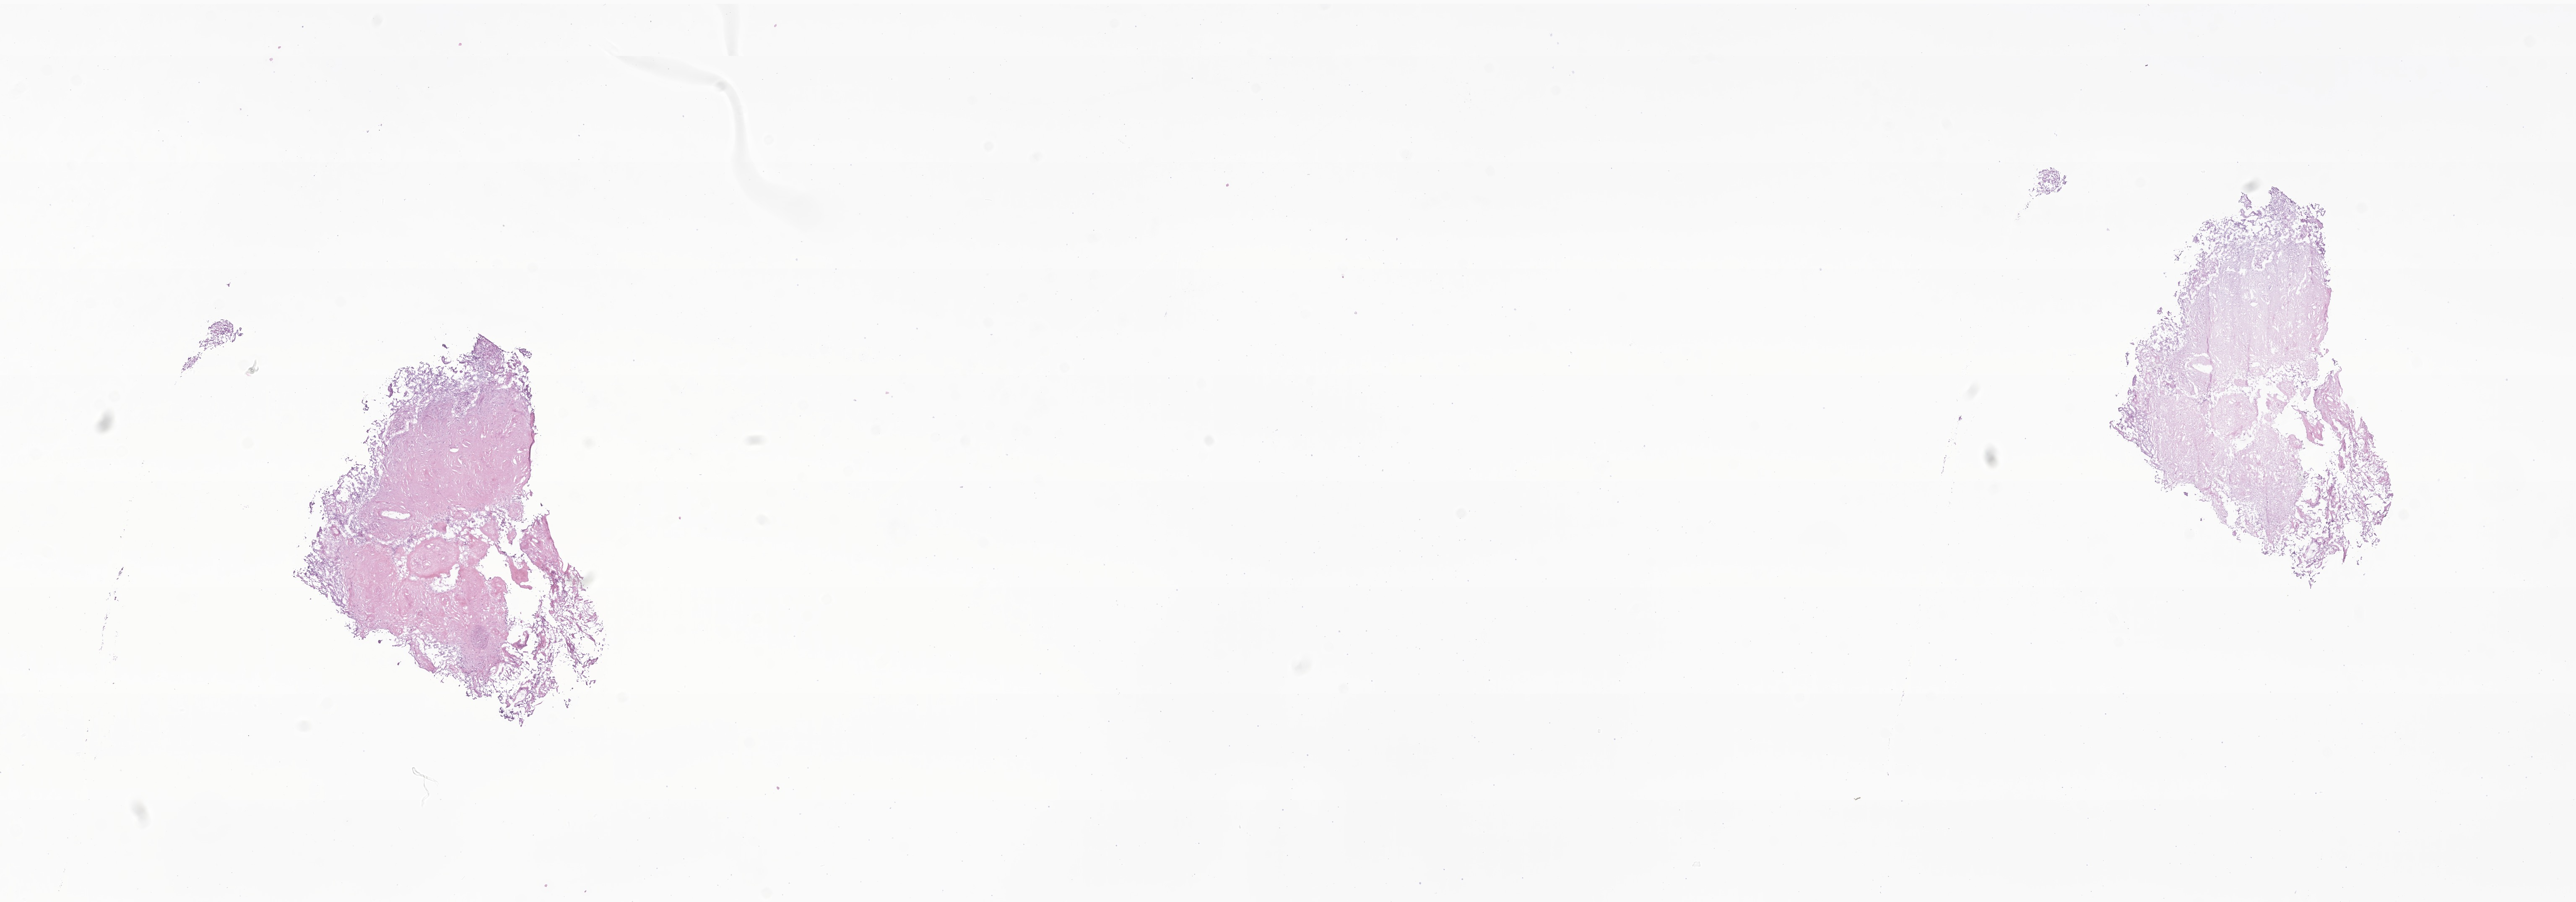
Whole-slide image, haematoxylin and eosin stain of tumor tissue from the brain, a low-resolution overview of the entire scanned area, about 25.9 x 9.1 mm. Male patient, age 75 months.
Specimen: cryosection (OCT / tissue freezing medium).